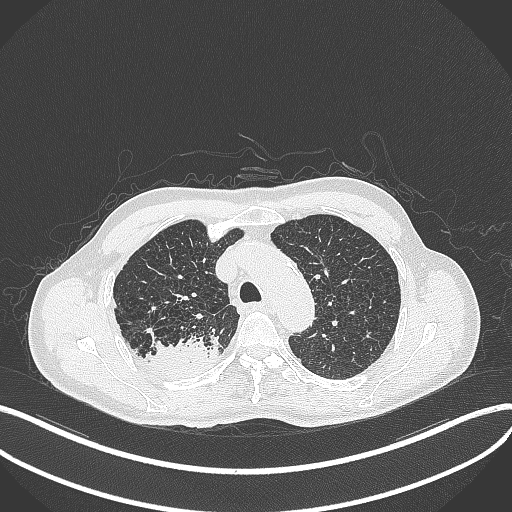
Chest CT, one axial slice. Position 336 of 428 along the scan axis. Lung window (W 1500 / L -600 HU). 512 × 512 image matrix, field of view 400 × 400 mm. Patient: male, 79 years. Case-level facts recorded for this patient, not image findings: clinical TNM (as recorded): T3 N0 M0.
Outlined on this slice (rectangle marked by the reading radiologist):
- lung tumour (recorded histology: adenocarcinoma): bounding box <139,336,223,378> (left, top, right, bottom; pixels)